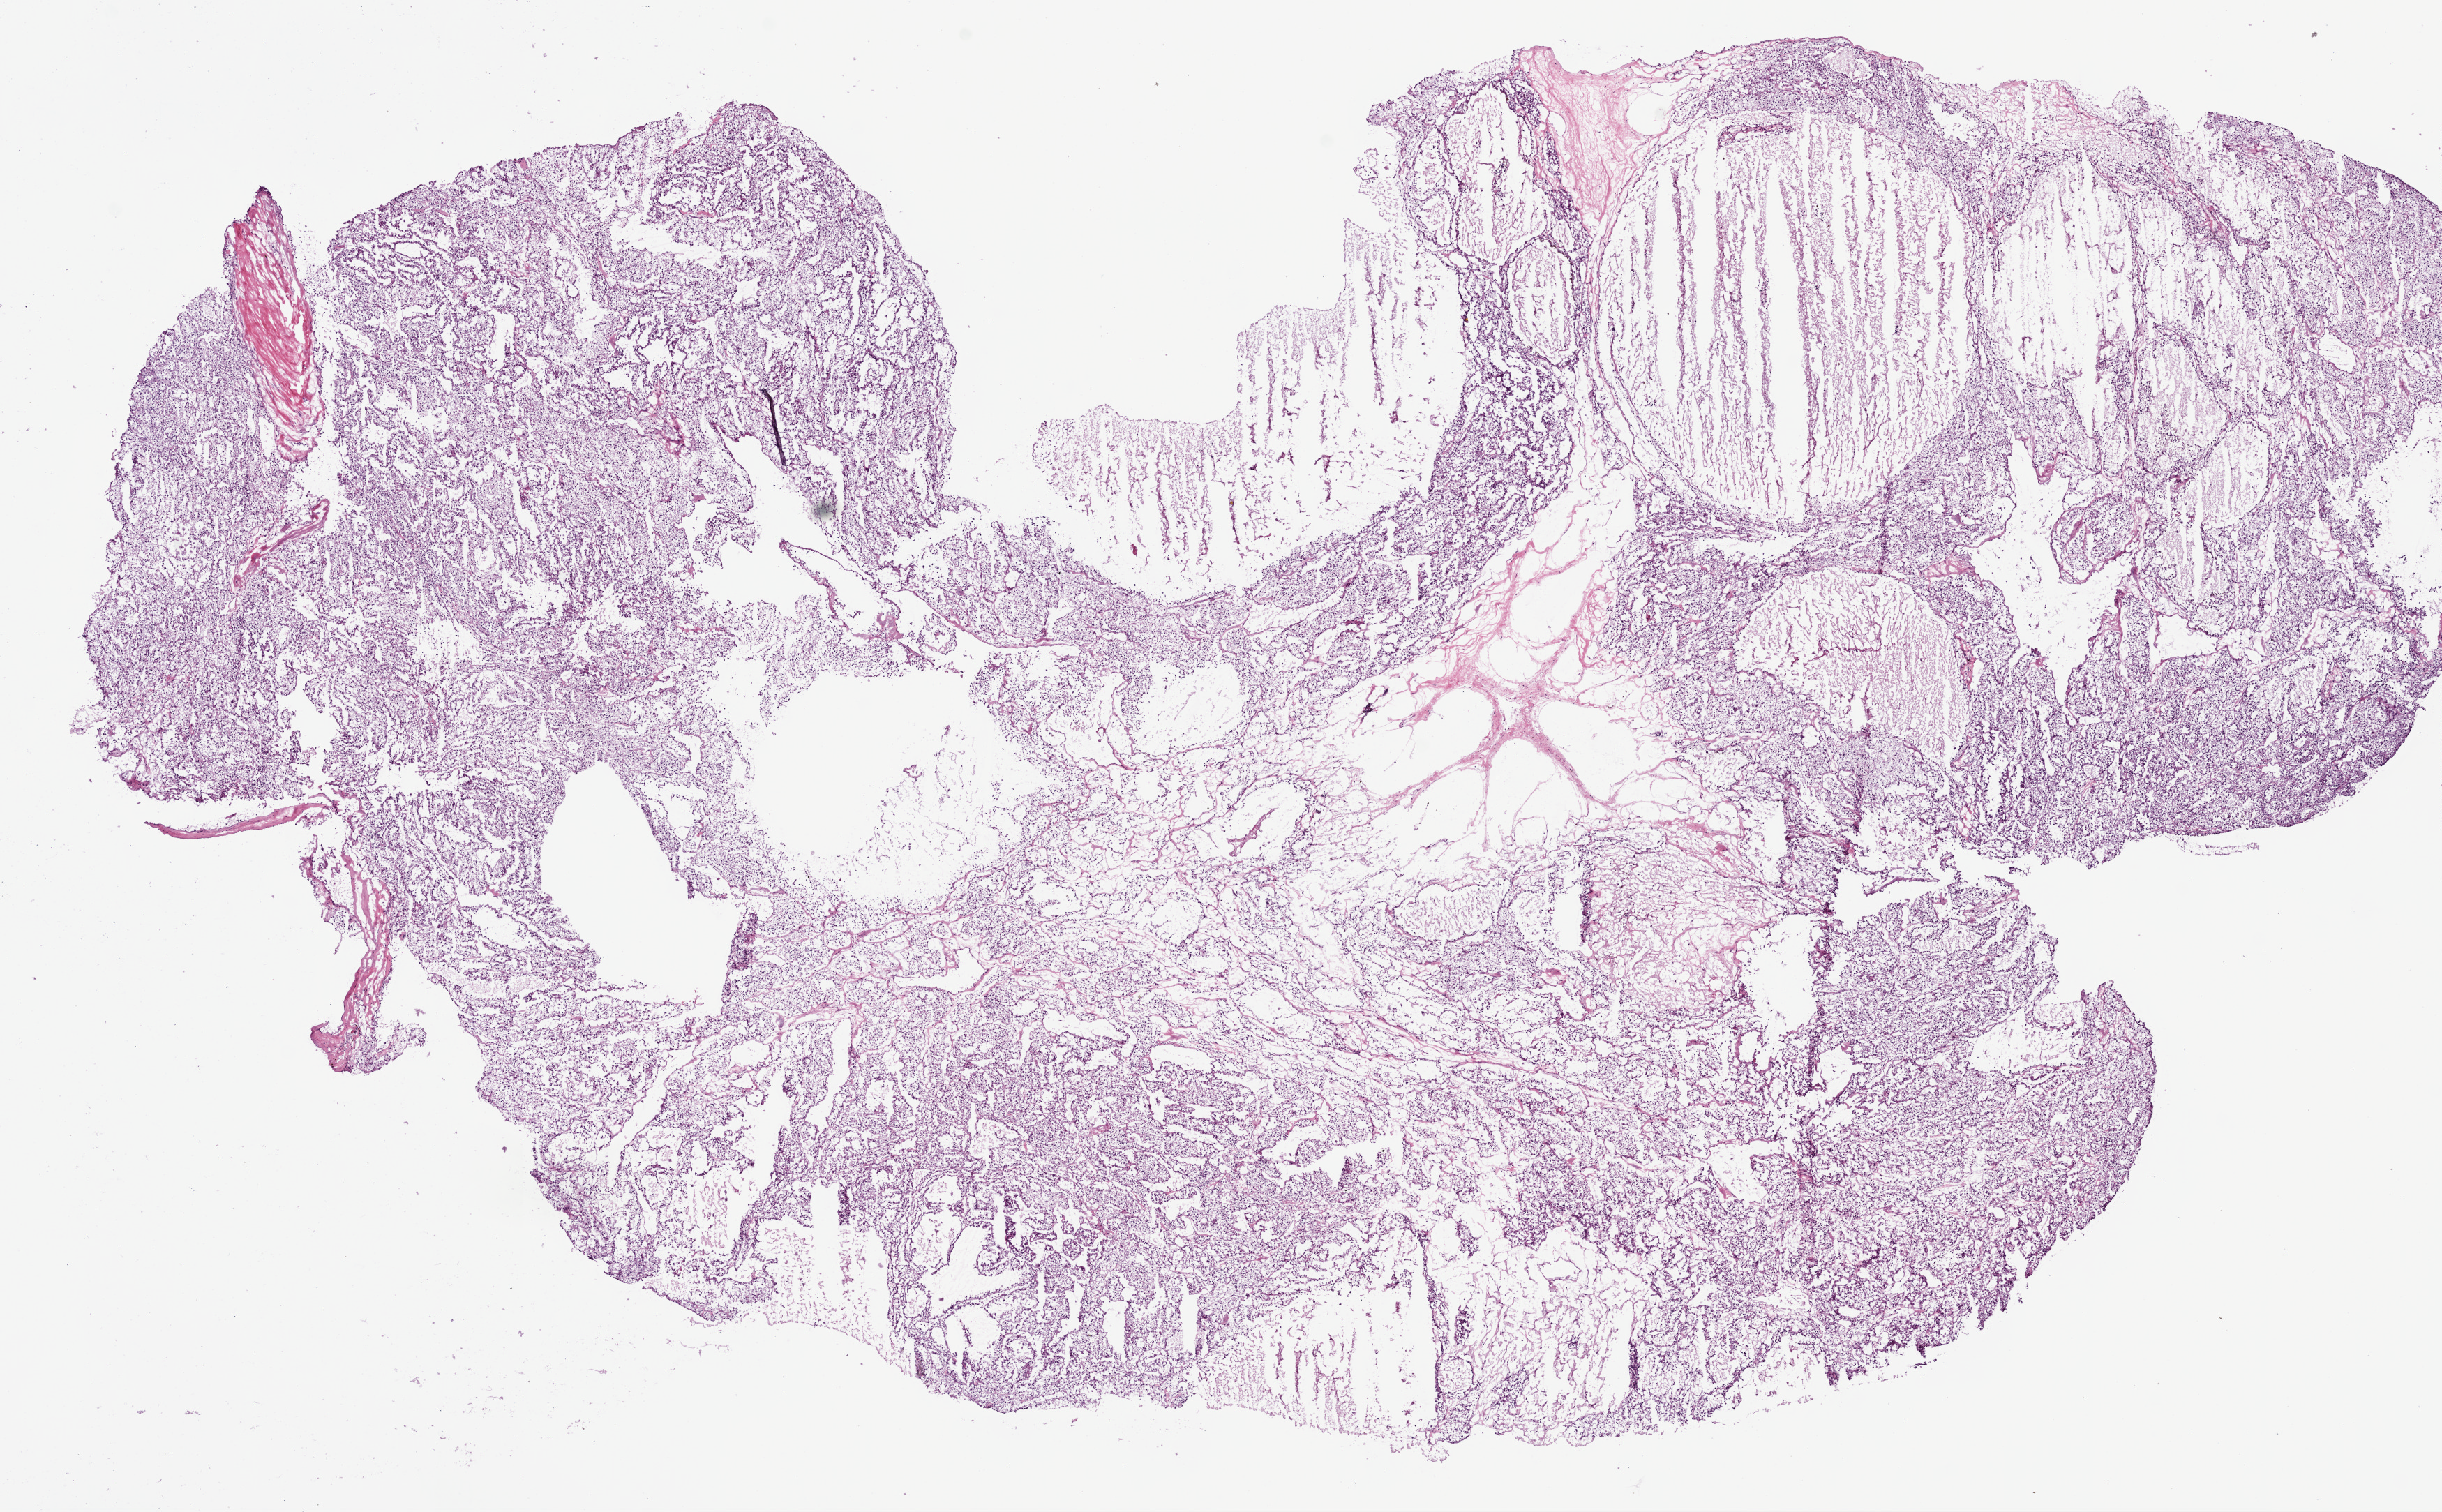
H&E-stained whole-slide image — a low-resolution overview of the entire scanned area, about 14.0 x 8.7 mm (from a 20x scan). Frozen section from the bottom of the tissue portion. Primary tumour sample from the kidney. Male, age 76 years at initial diagnosis. Histologic grade: G2 (moderately differentiated). Composition of this section per pathologist review: tumour cells 85%, tumour nuclei 85%, normal cells 0%, stromal cells 15%, necrosis 0%.
AJCC pathologic stage: II. Histologic diagnosis: Clear cell adenocarcinoma, NOS.